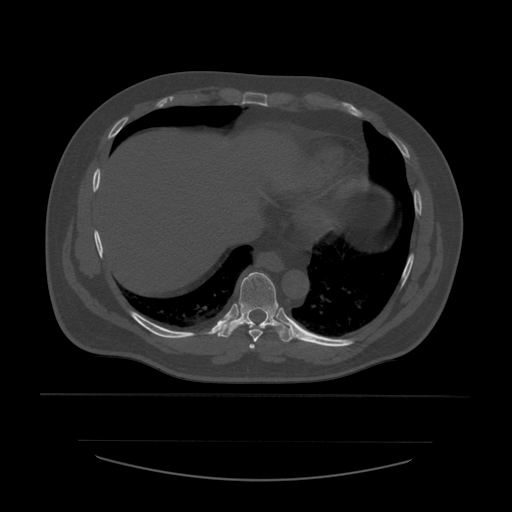
CT including the spine, one axial slice. Slice 324 of 532 in the series (ordered by position). 120 kVp. Bone window (W 1800 / L 400 HU). 1.25 mm slice thickness. 512 × 512 image matrix. Patient age 44 years. From the clinical record (not read from this slice): primary cancer: soft tissue sarcoma.
Outlined on this slice (semi-automatic segmentation, software-assisted and operator-edited):
- T7 vertebra: bounding box [x1, y1, x2, y2] px = [249, 344, 255, 350]
- T8 vertebra: [249, 329, 263, 342]
- T9 vertebra: [217, 272, 297, 342]